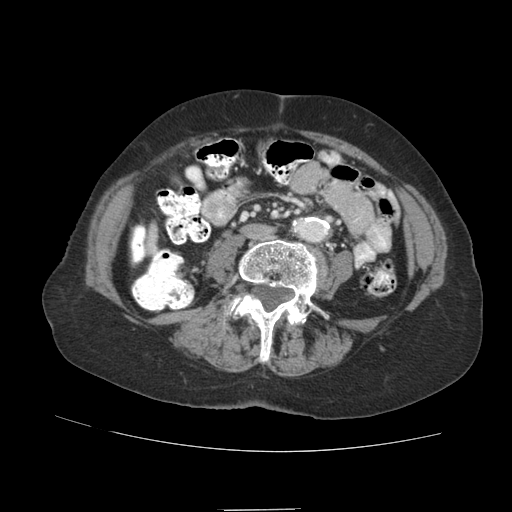
Contrast-enhanced abdominal CT (liver protocol), one axial slice; position 6 of 89 along the scan axis; reconstruction kernel STANDARD; soft-tissue window (W 400 / L 40 HU); 2.5 mm slice thickness; 512 × 512 image matrix, field of view 360 × 360 mm. Case-level facts recorded for this patient, not image findings: diagnosis: hepatocellular carcinoma (patient treated with transarterial chemoembolisation; whether this scan precedes or follows treatment is not stated here); TNM stage (as recorded): Stage-II; Child-Pugh class: A; tumour nodularity: multinodular; tumour size: 4 cm.
Structures marked on this image (semi-automatically segmented with operator editing):
- liver parenchyma outside the tumour (the mass and vessels are separate outlines, so this box may not span the whole liver): bounding box <131,226,144,258> (left, top, right, bottom; pixels)
- liver vessels: <132,227,144,257>